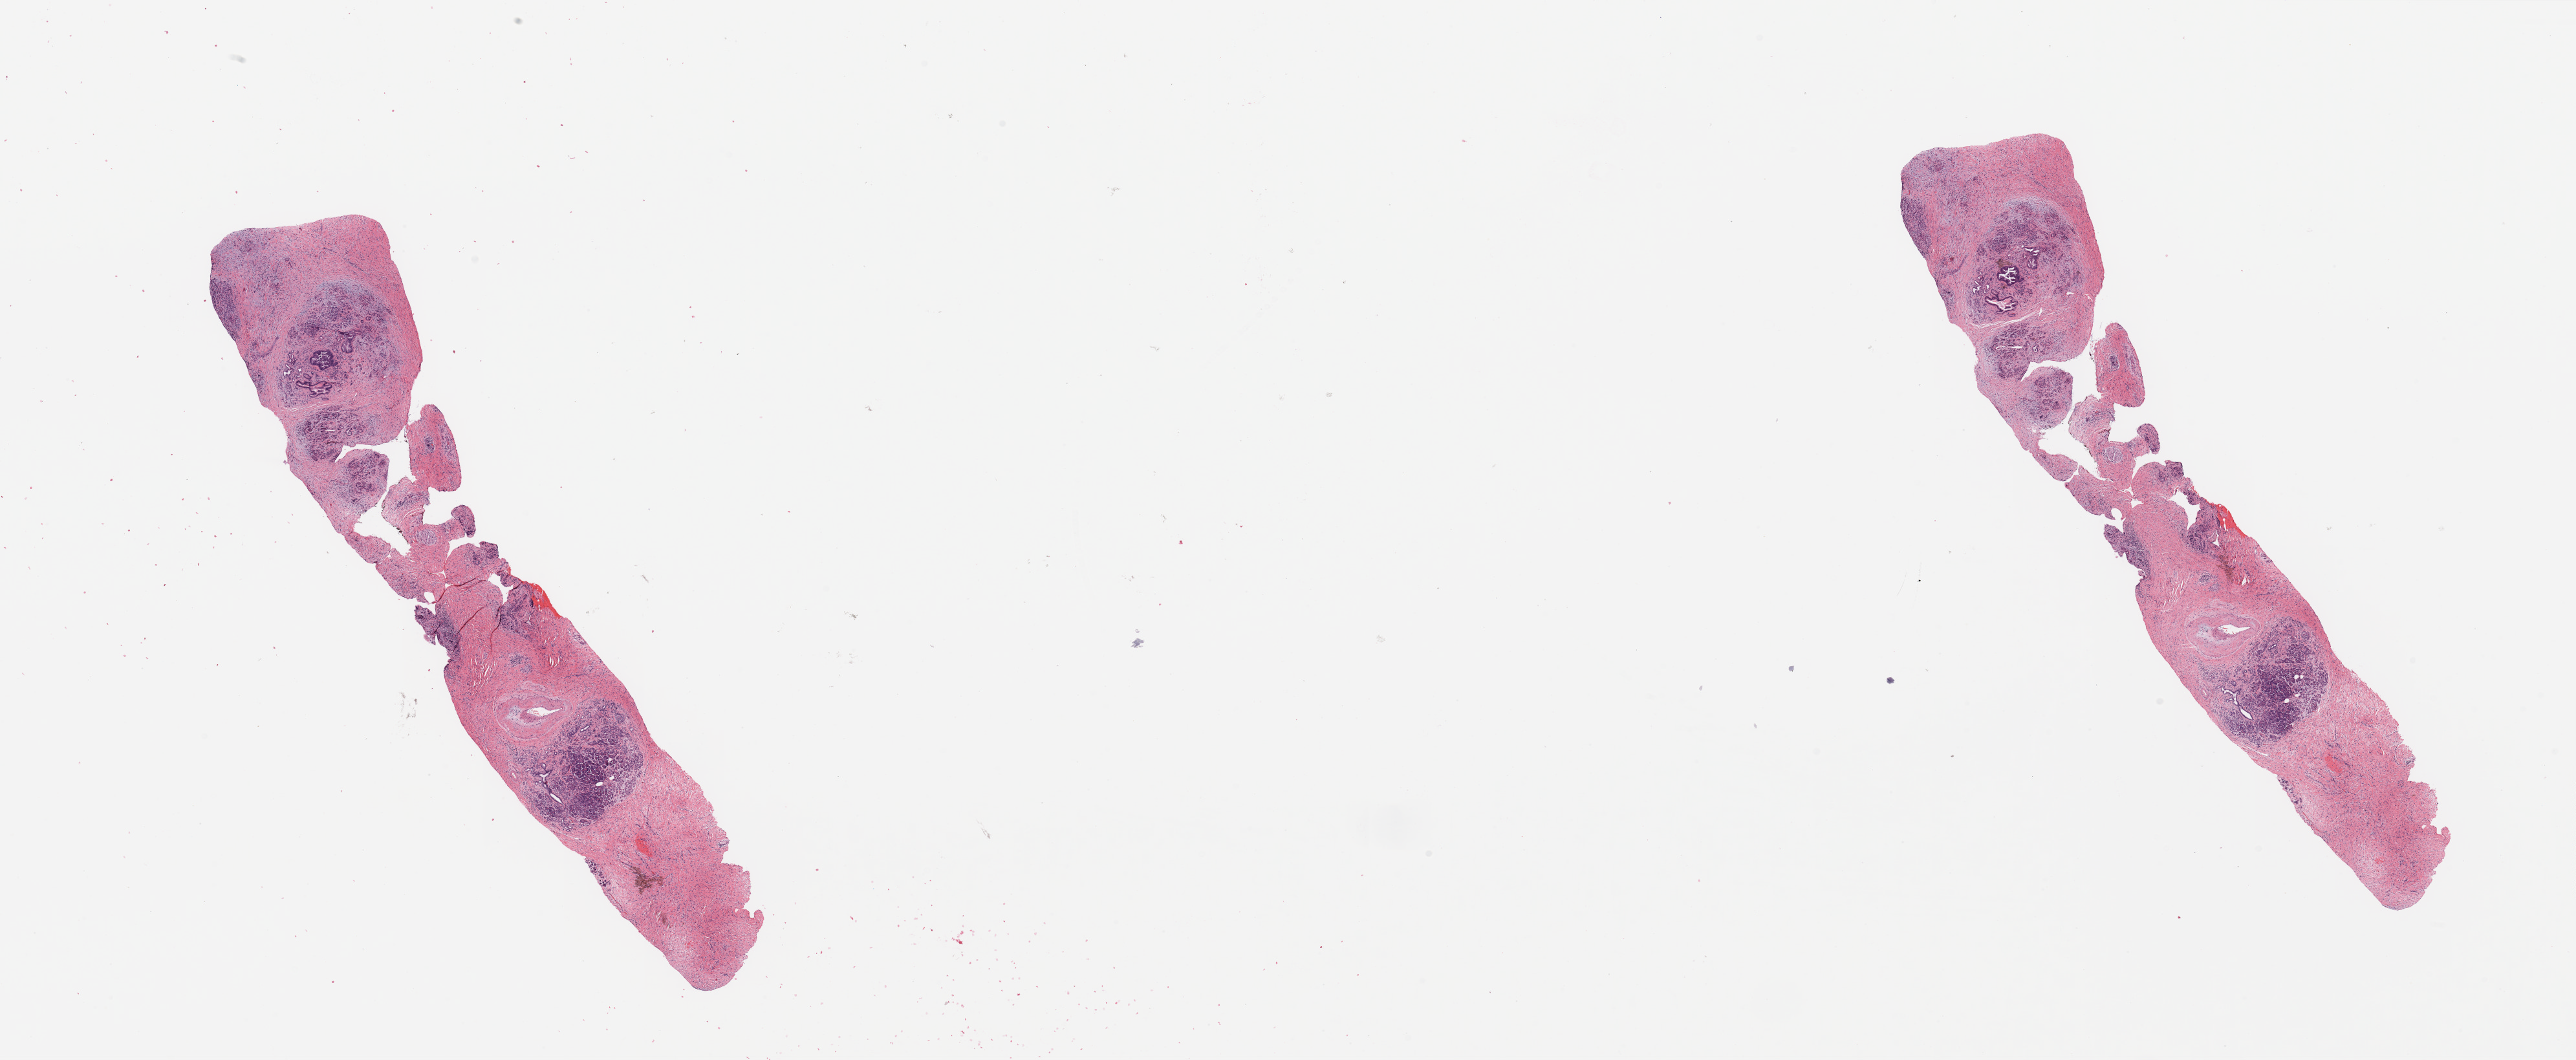
Whole-slide histology image, H&E — low-resolution overview of the scanned area, about 31.5 x 13.0 mm (slide scanned at 20x). Tumour tissue sample, sampled site: pancreas. Male, 80 y/o. Histologic grade: G2 (moderately differentiated). Composition of this section per pathologist review: tumour nuclei 5%, necrosis 0%.
- AJCC pathologic stage: IIB
- primary tumour site (as recorded): head
- diagnosis: Infiltrating duct carcinoma, NOS